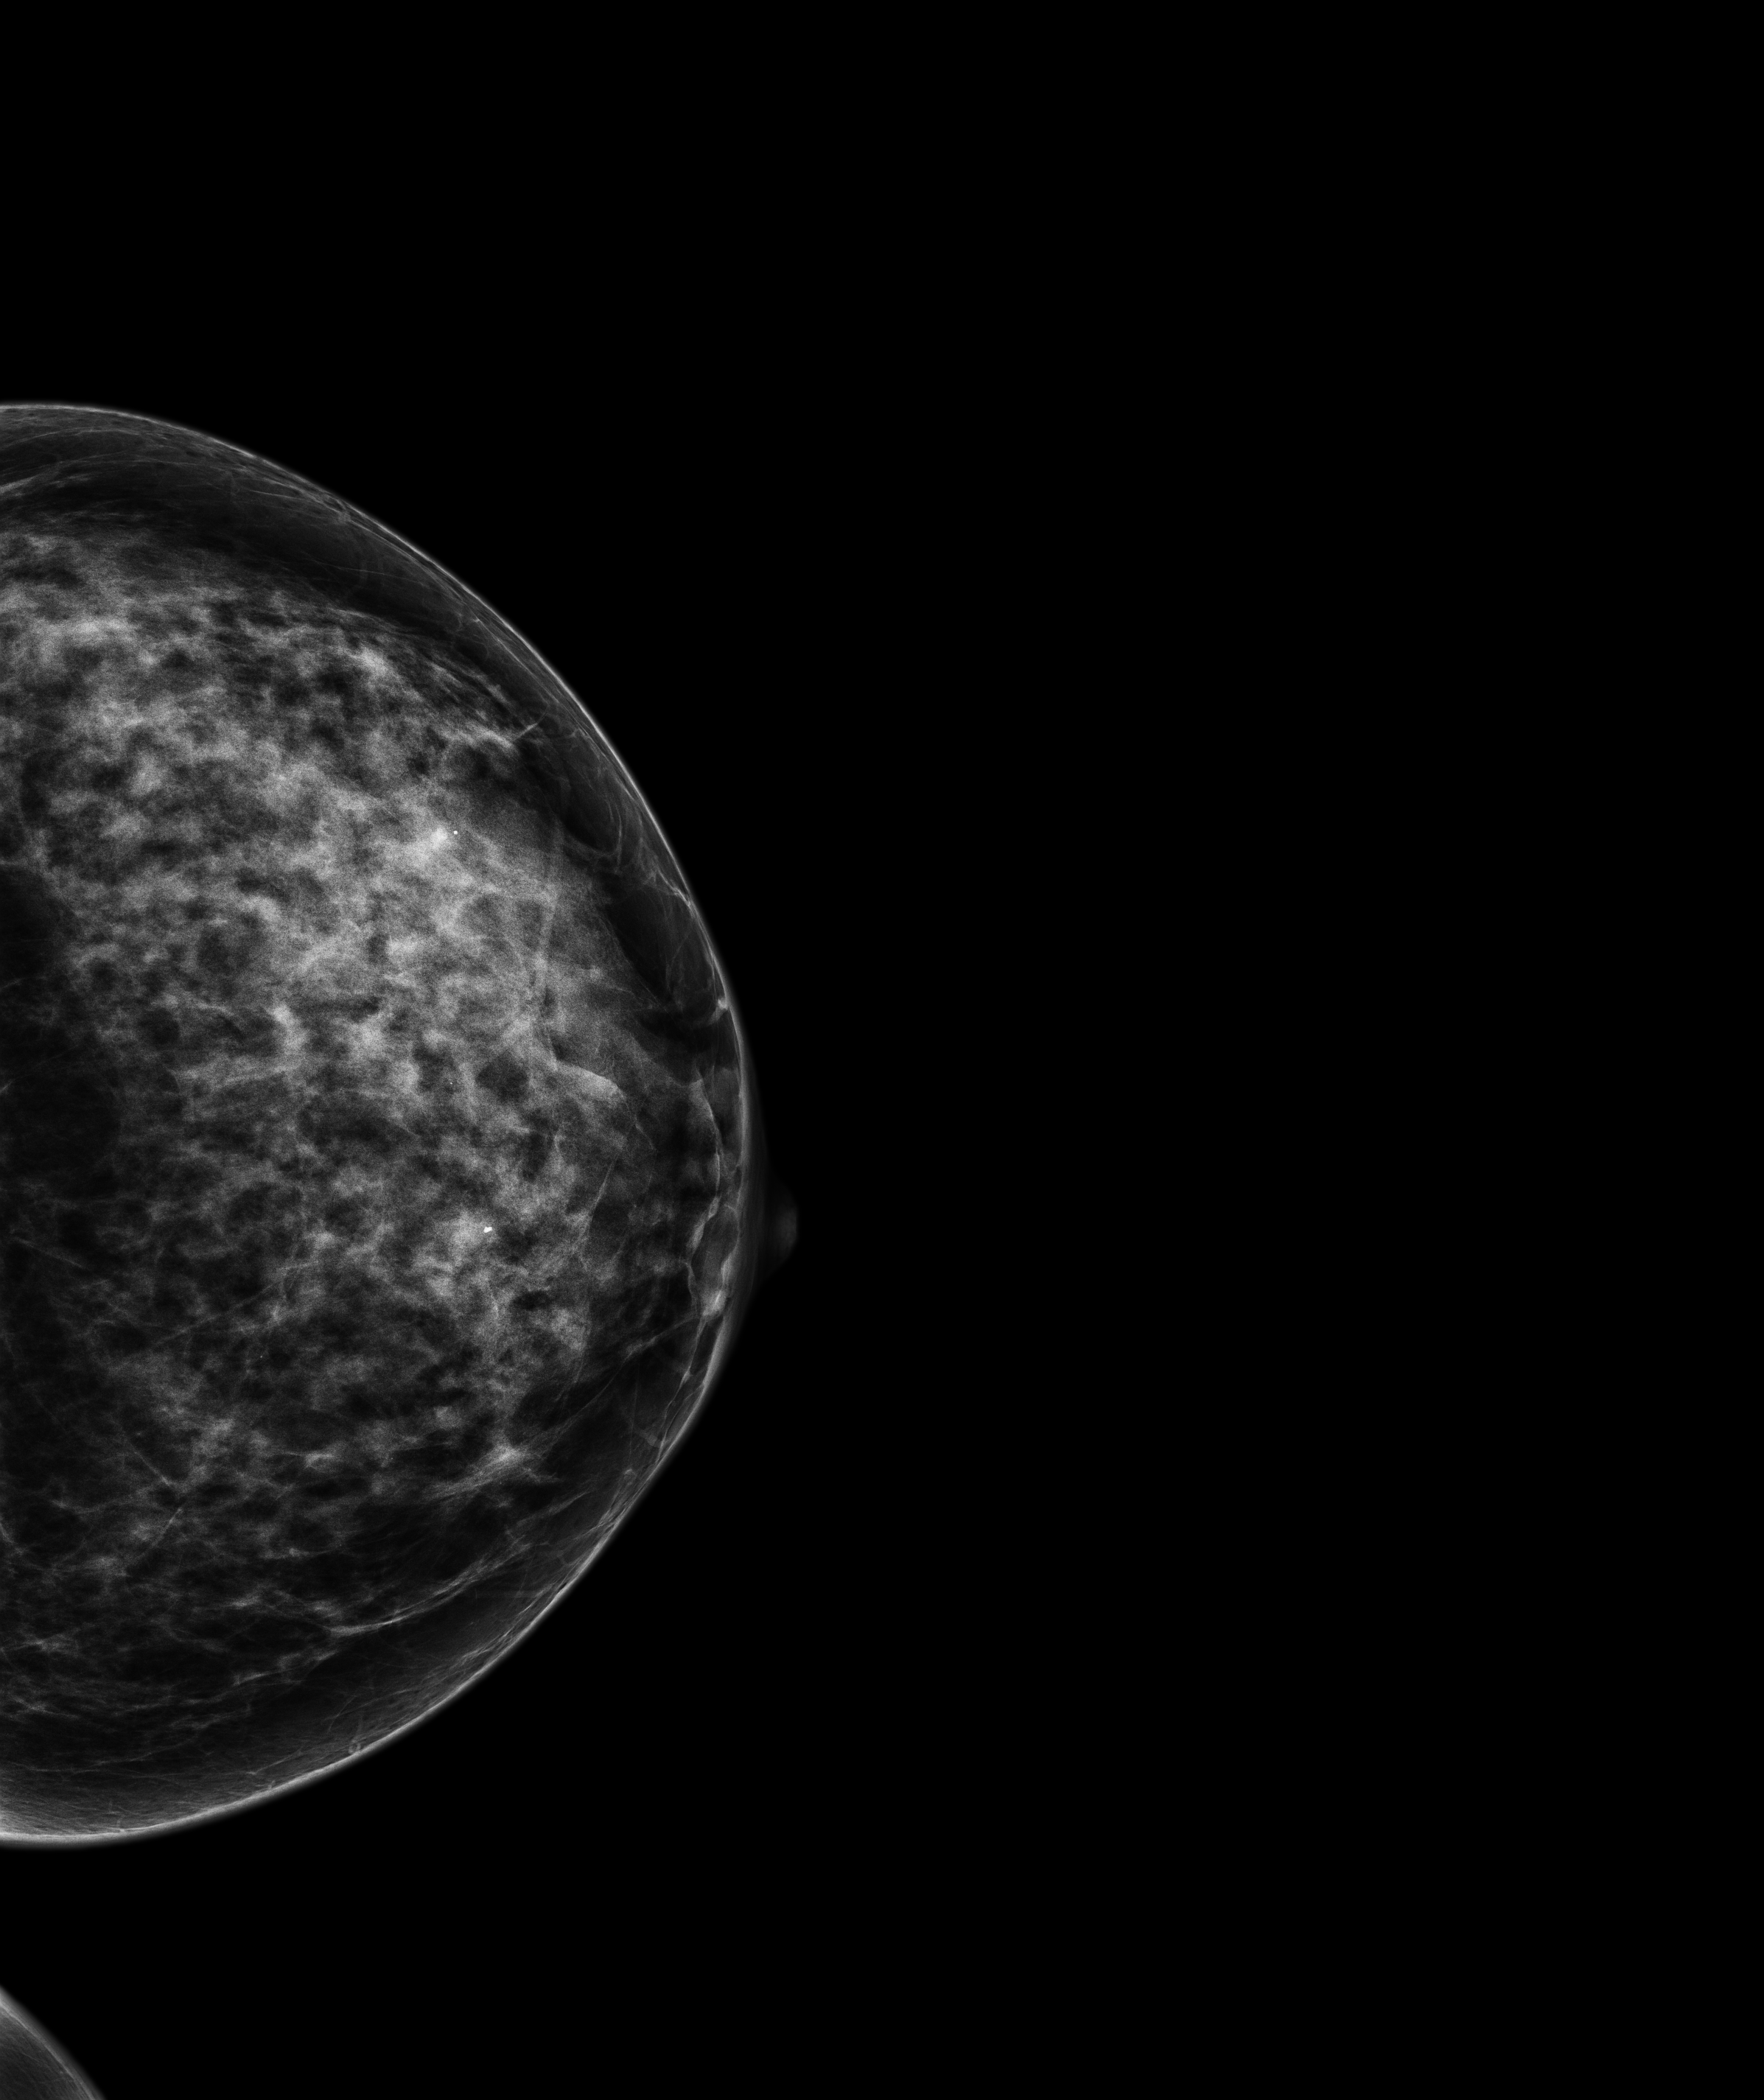
Digital mammogram (FFDM); left breast; CC view; screening examination; compressed breast thickness 59.3 mm; system: Senographe Pristina. Female patient, age 42 years.
- breast density at the screening exam (both breasts): extremely dense (BI-RADS density category d)
- final BI-RADS category for the screening round (tomosynthesis exam, both breasts): category 1
- recall: no recall after this screen